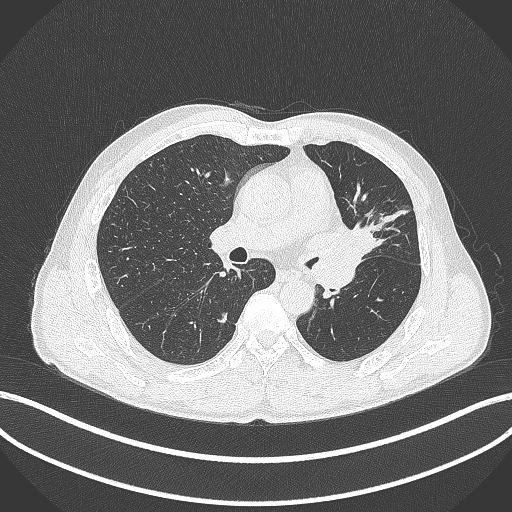
Chest CT, one axial slice; position 240 of 429 along the scan axis; lung window (W 1500 / L -600 HU); 1 mm slice thickness; 512 × 512 image matrix, field of view 400 × 400 mm. Patient: male, 57 years. Case-level facts recorded for this patient, not image findings: clinical TNM (as recorded): T2b N0 M0.
Outlined on this slice (bounding box drawn by a radiologist):
- lung tumour (recorded histology: squamous cell carcinoma): bounding box (x1, y1, x2, y2) in pixels: (320, 221, 383, 262)